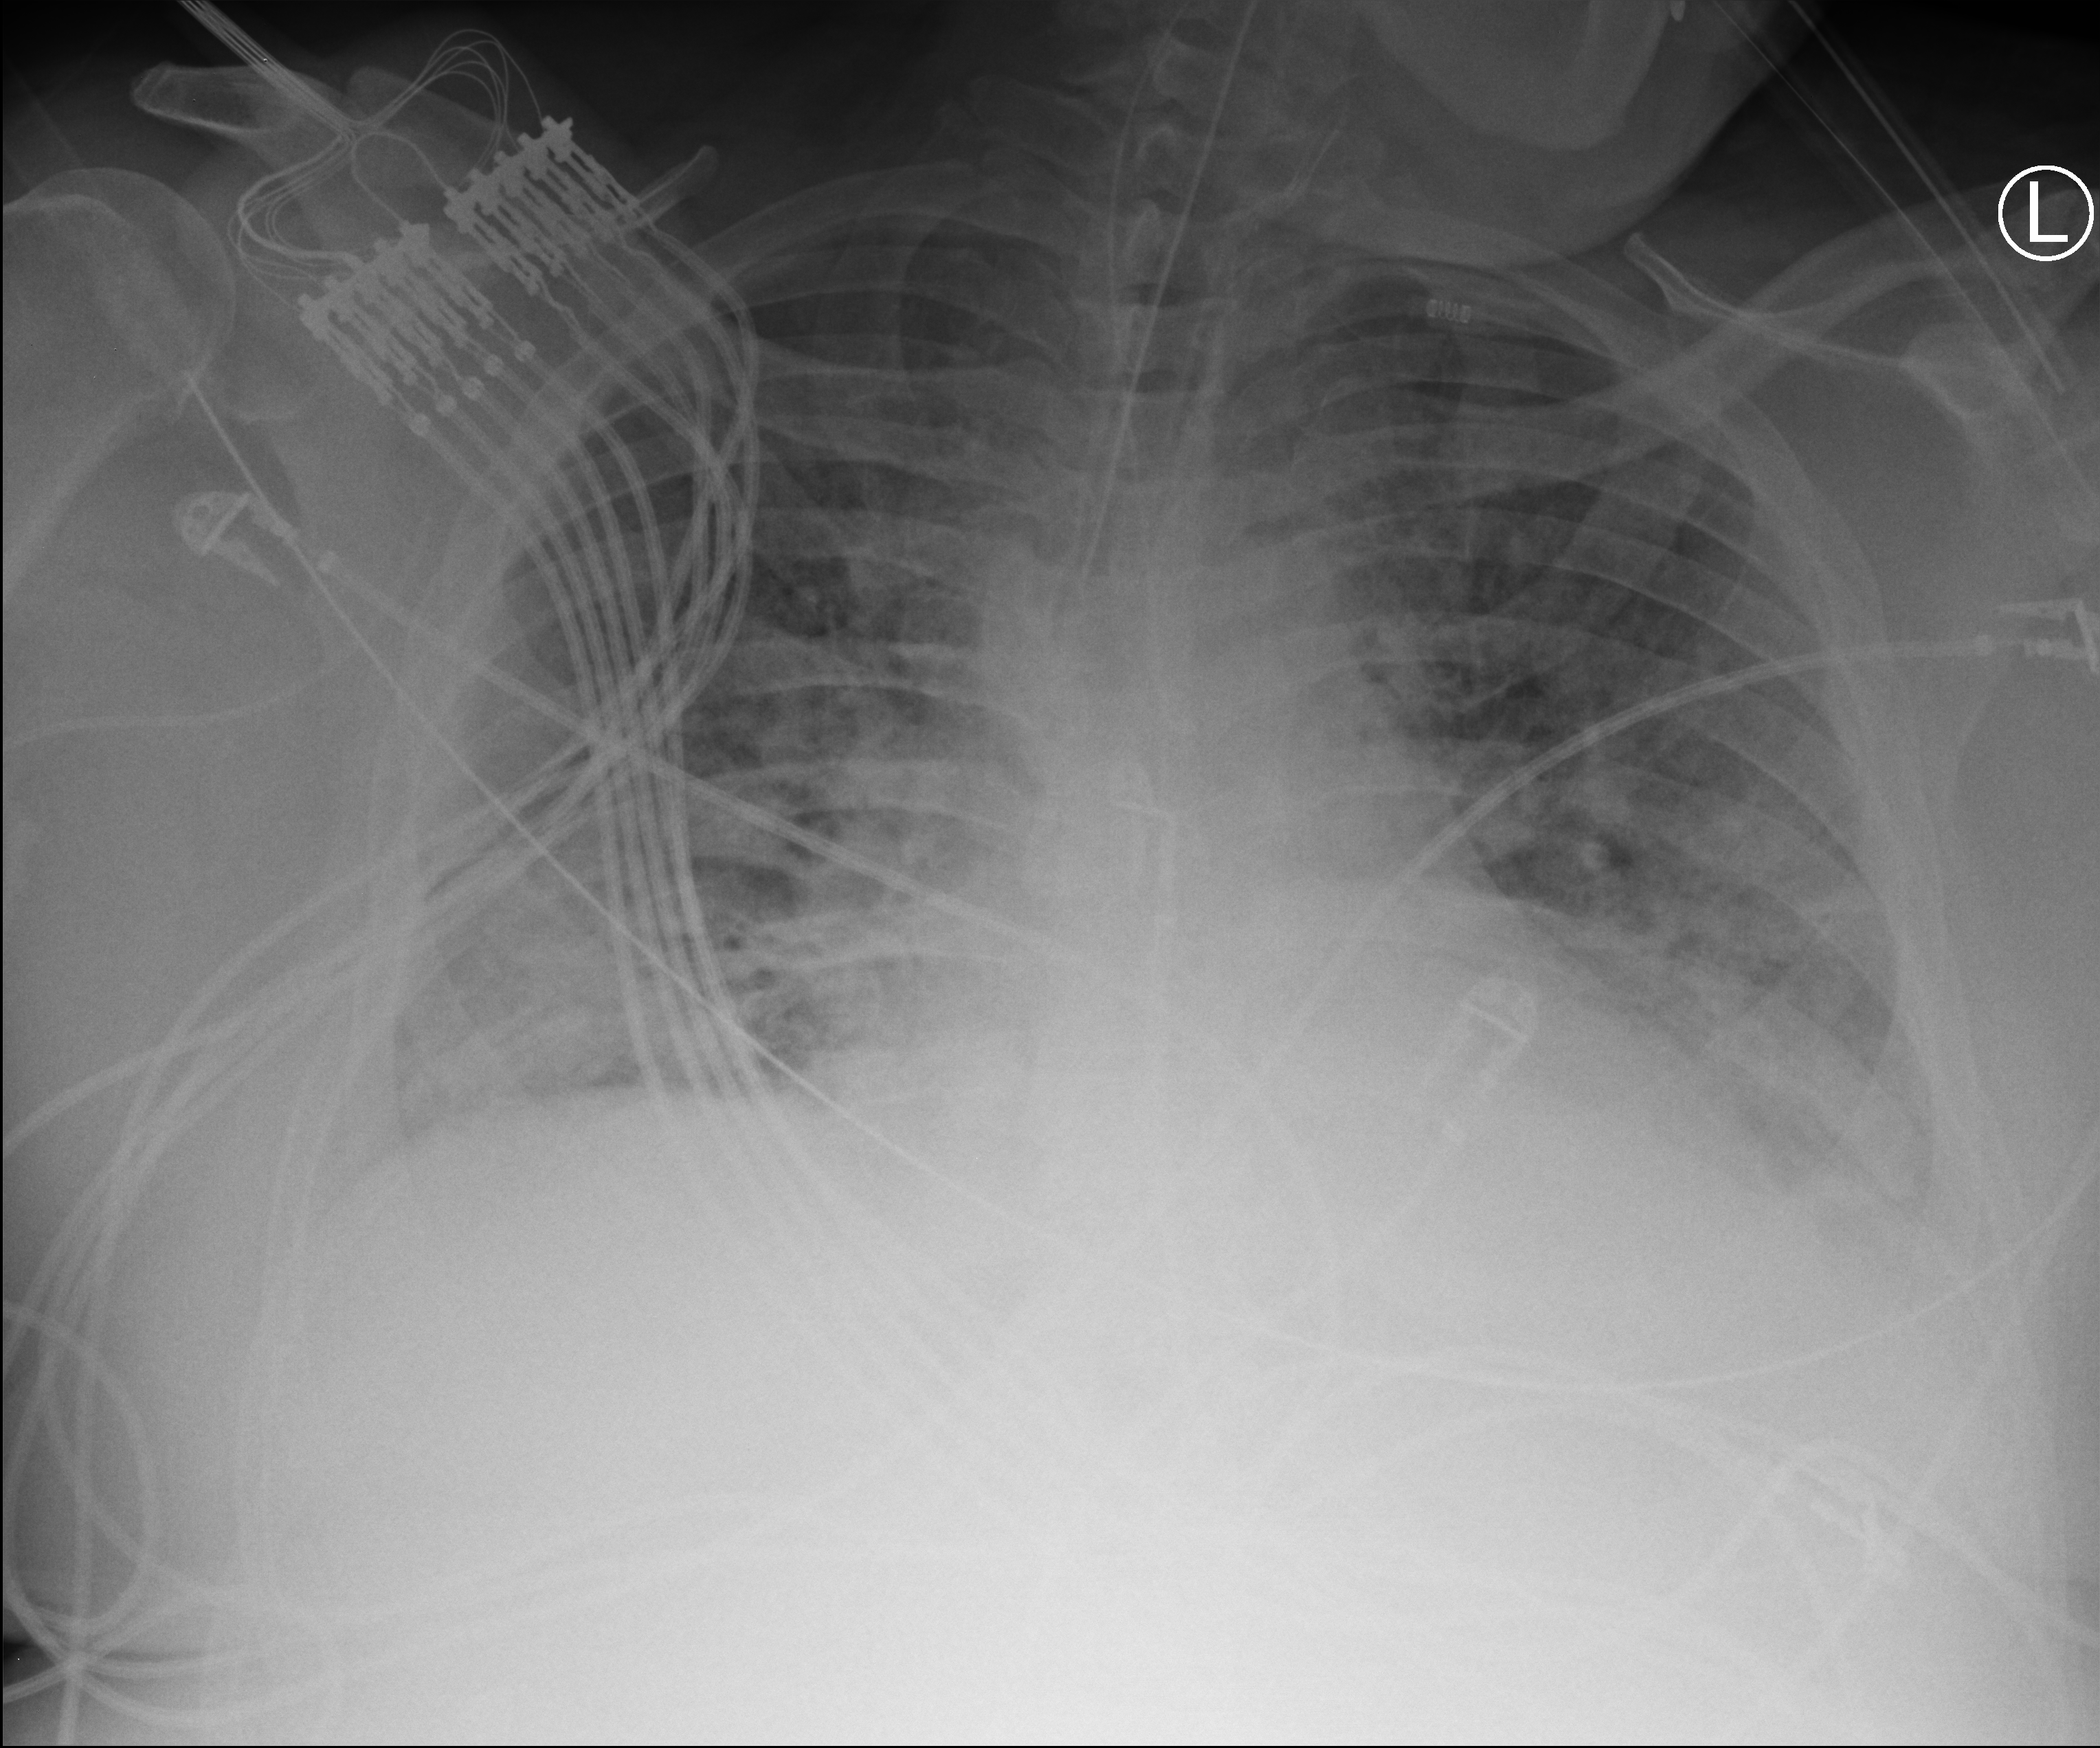
Chest X-ray (portable), anteroposterior (AP) projection. Male patient hospitalised with COVID-19, age 60–74 years.
From the hospital-stay record, not from the radiograph (when in the stay this image was taken is not recorded): hypertension (admission record): yes; length of hospital stay: 34 days.